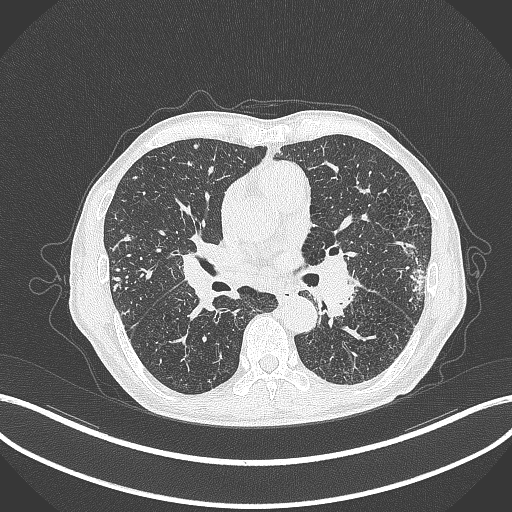
Chest CT, one axial slice; reconstruction kernel B70f; 120 kVp; lung window (W 1500 / L -600 HU); 1 mm slice thickness; 512 × 512 image matrix, field of view 400 × 400 mm. Male patient, age 74 years. From the clinical record (not read from this slice): clinical TNM (as recorded): T2a N1 M0.
Outlined on this slice (bounding box drawn by a radiologist):
- lung tumour (recorded histology: adenocarcinoma): bounding box [x1, y1, x2, y2] px = [398, 236, 423, 262]